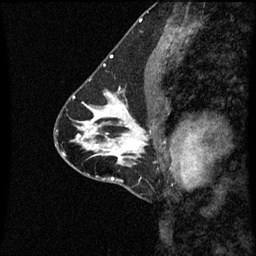
Breast MRI (dynamic contrast-enhanced), one sagittal slice. Slice 30 of 60 in the series (ordered by position). Dynamic contrast-enhanced series, image 2 of 3 at this slice position (ordered by acquisition). 1.5 T. TE 4.2 ms, TR 8.9 ms. 256 × 256 image matrix. Female patient, age 43 years. From the clinical record (not read from this slice): setting: breast cancer imaged before/during neoadjuvant chemotherapy; receptor status: HR-positive, HER2-negative.
Outlined on this slice (semi-automatically segmented with operator editing):
- analysis volume of interest (the breast-tissue region the enhancement analysis was run in; not a lesion): bounding box [x1, y1, x2, y2] px = [110, 100, 161, 163]
- tumour enhancement mask (voxels above the 70 % enhancement threshold inside the analysis volume of interest): [110, 106, 144, 153]